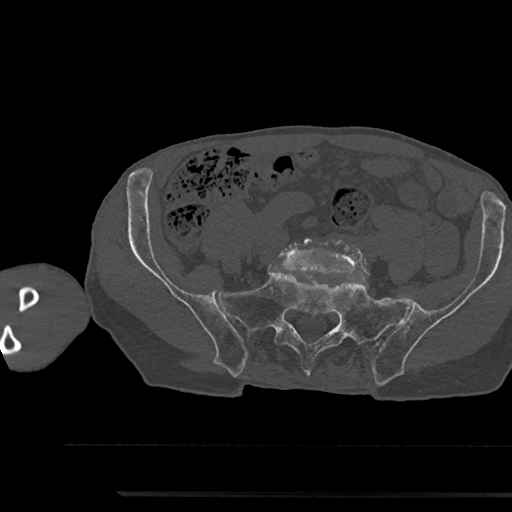
CT including the spine, one axial slice. Position 300 of 797 along the scan axis. Reconstruction kernel Br40s/3. 120 kVp. Bone window (W 1800 / L 400 HU). 512 × 512 image matrix. Male patient, age 79 years. From the clinical record (not read from this slice): primary cancer: prostate.
Structures marked on this image (semi-automatic segmentation, software-assisted and operator-edited):
- L5 vertebra: bounding box <280,237,368,275> (left, top, right, bottom; pixels)